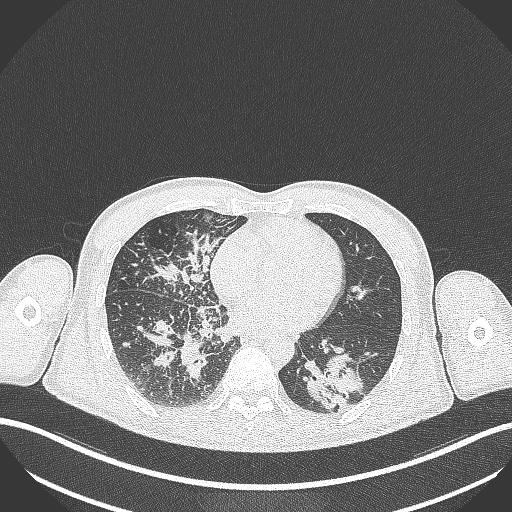
Chest CT, one axial slice. Slice 125 of 348 in the series (ordered by position). Reconstruction kernel B70f. 120 kVp. Lung window (W 1500 / L -600 HU). 512 × 512 image matrix. Patient: male, 49 years. Case-level facts recorded for this patient, not image findings: clinical TNM (as recorded): T2b N1 M0.
Outlined on this slice (bounding box drawn by a radiologist):
- lung tumour (recorded histology: adenocarcinoma): box from (x=298, y=350) to (x=365, y=410) px